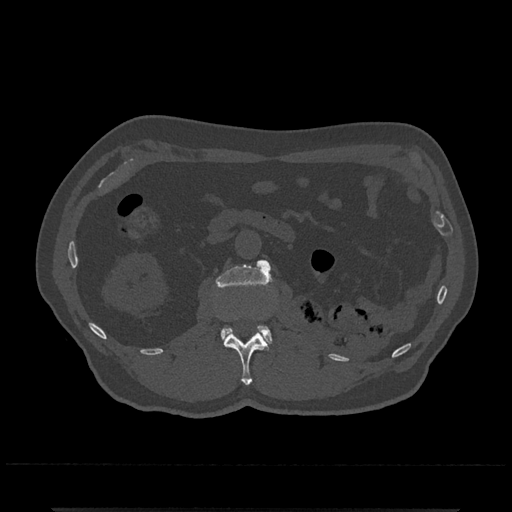
CT including the spine, one axial slice; position 332 of 797 along the scan axis; reconstruction kernel Br40s/3; 120 kVp; bone window (W 1800 / L 400 HU); 0.5 mm slice thickness; 512 × 512 image matrix, field of view 393 × 393 mm. Patient: male, 67 years. Case-level facts recorded for this patient, not image findings: primary cancer: prostate.
Annotated regions visible in this slice (semi-automatic segmentation, software-assisted and operator-edited):
- L1 vertebra: box from (x=224, y=332) to (x=269, y=385) px
- L2 vertebra: (x=216, y=260)–(x=272, y=345)